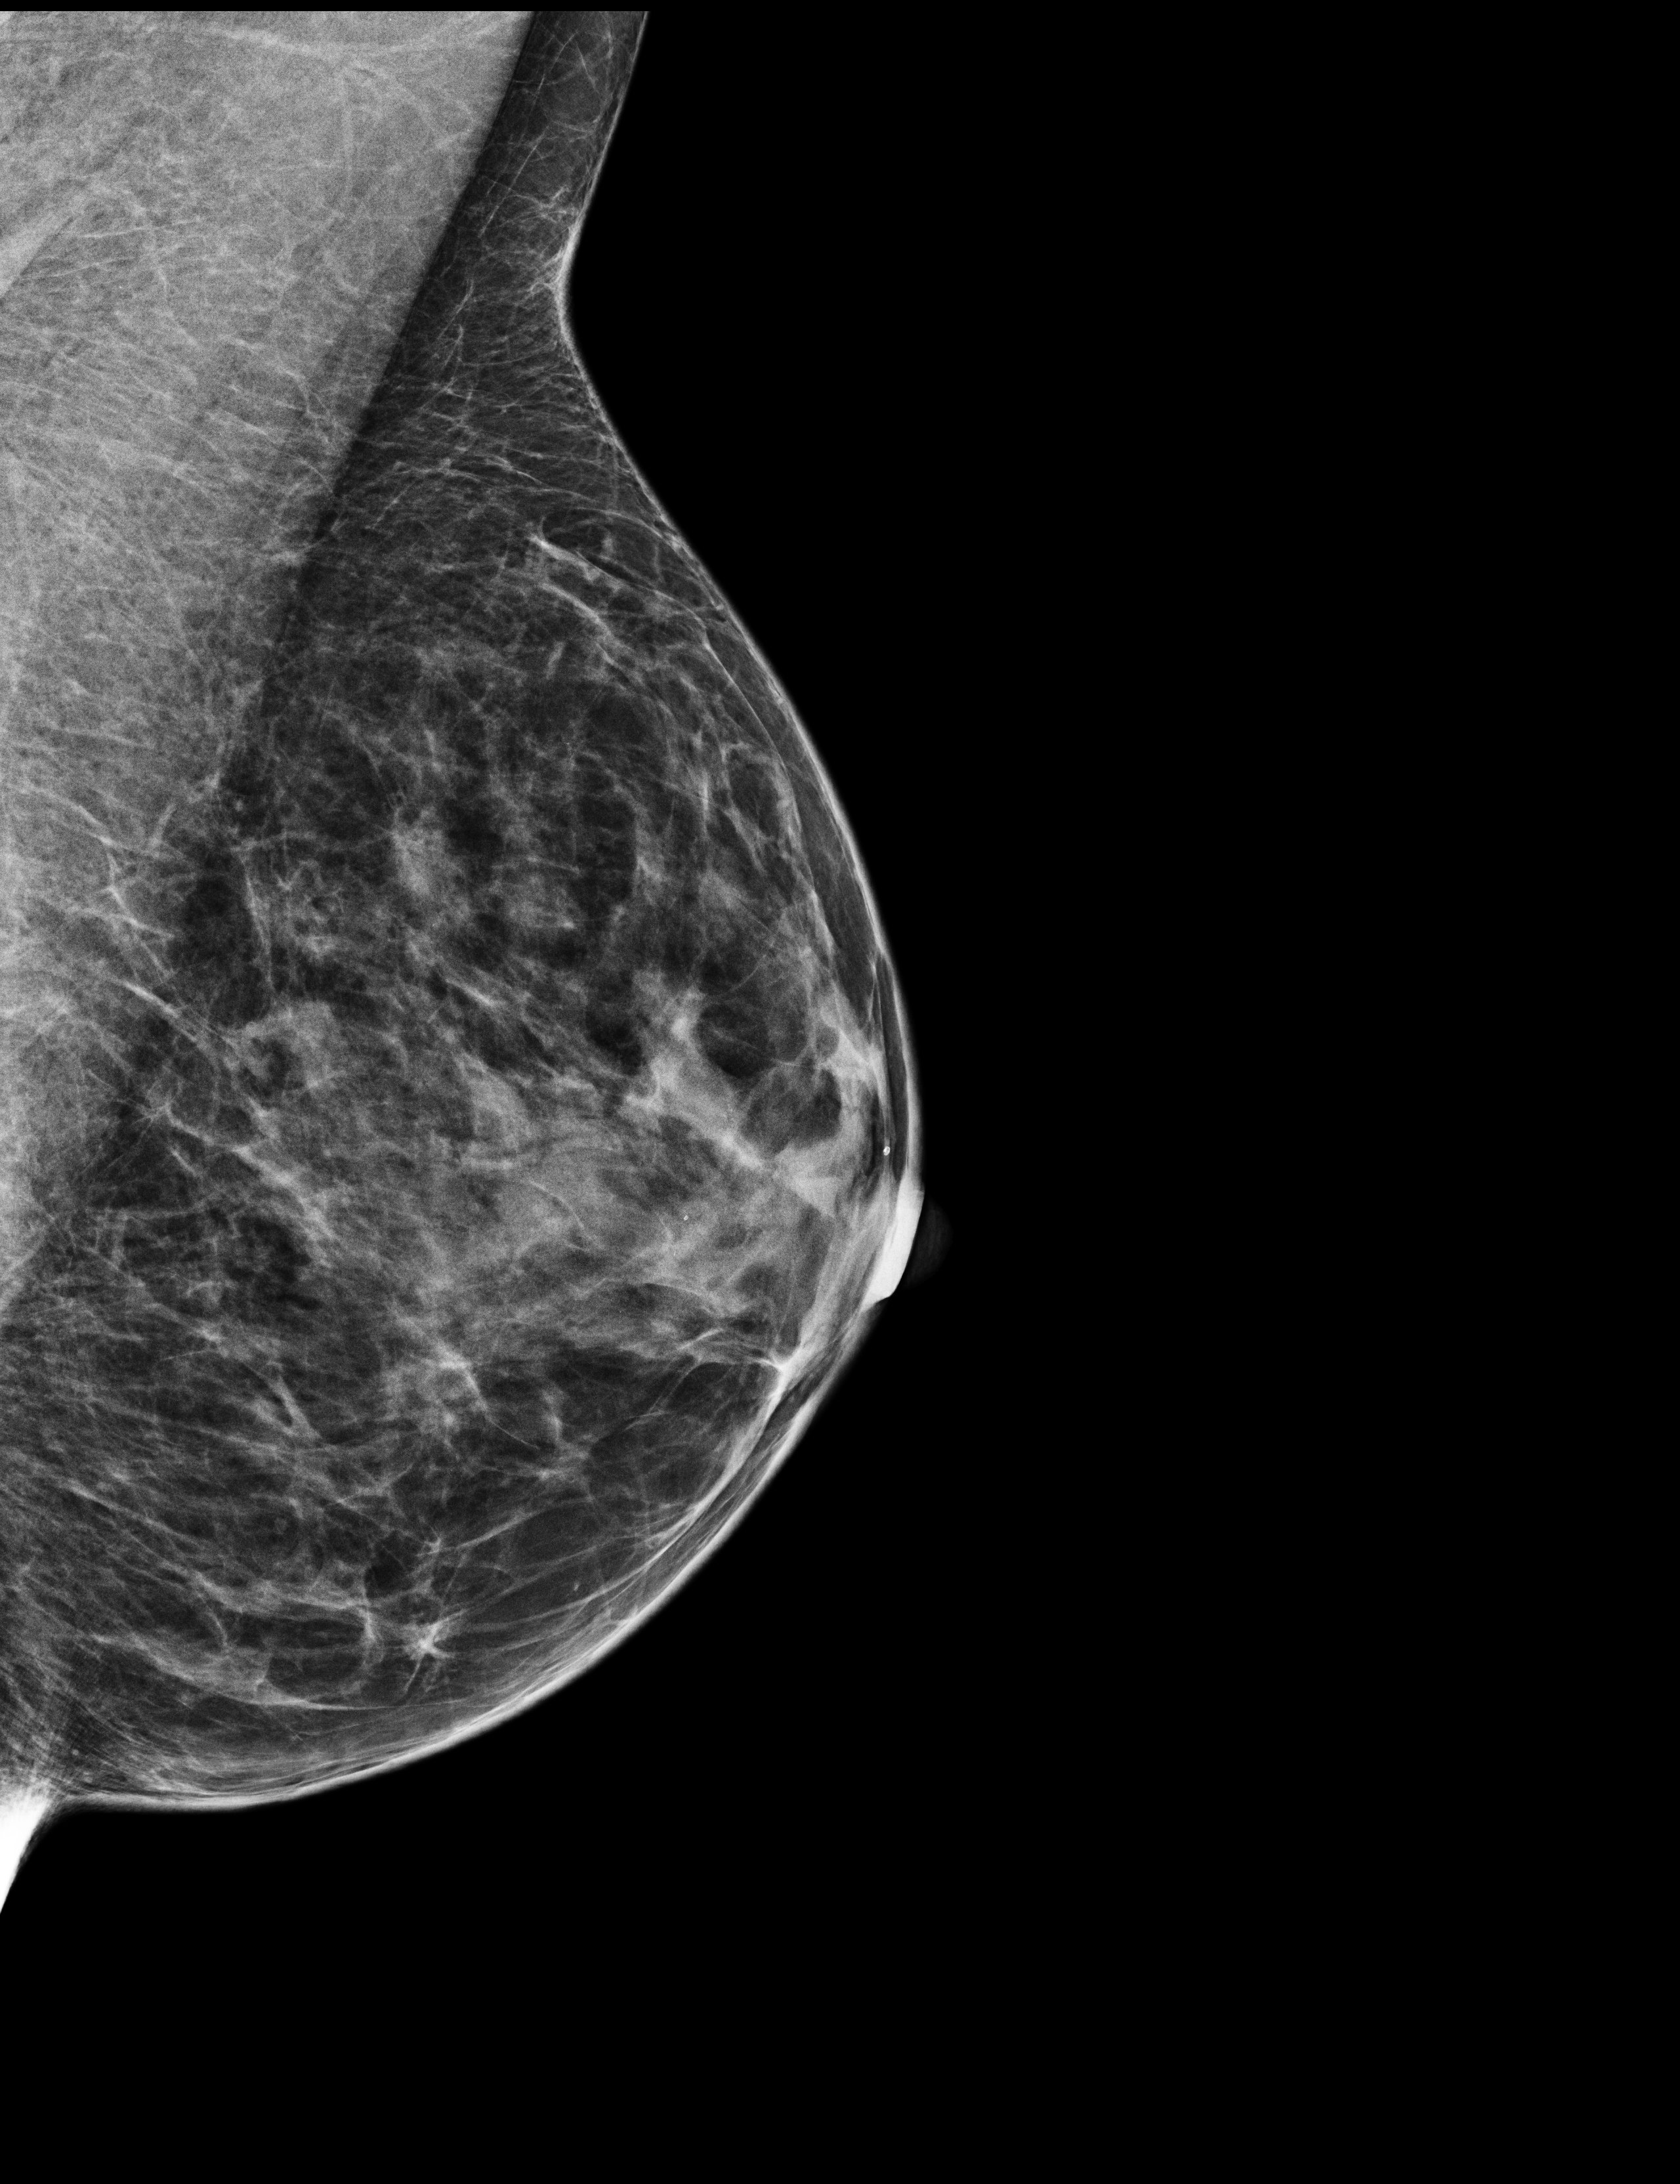
Annual screening mammography examination, compressed breast thickness 45 mm. Patient aged 47 years (female).
Image type: full-field digital mammogram. Breast: left. Projection: medio-lateral oblique projection.